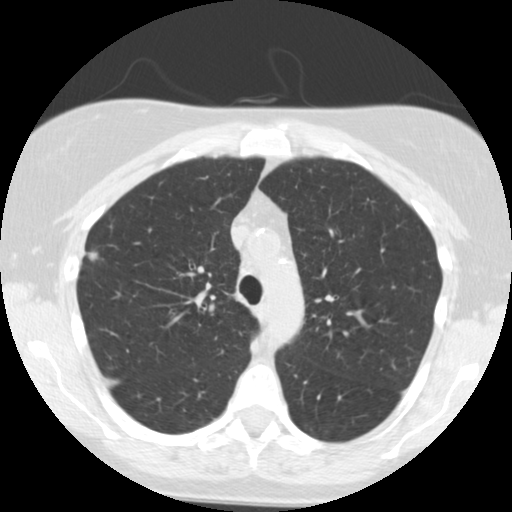
Low-dose screening chest CT, axial slice. Second screening round (one year after baseline). Lung window (W 1500 / L -600 HU). Standard (soft-tissue) reconstruction kernel (STANDARD). Slice 172 of 244 in the series. Female participant, aged 55 years at enrolment.
Expert-annotated lung lesion, bounding box [x1, y1, x2, y2] px = [68, 238, 116, 275]. Screening reader's record for this exam: no non-calcified nodule ≥4 mm recorded.